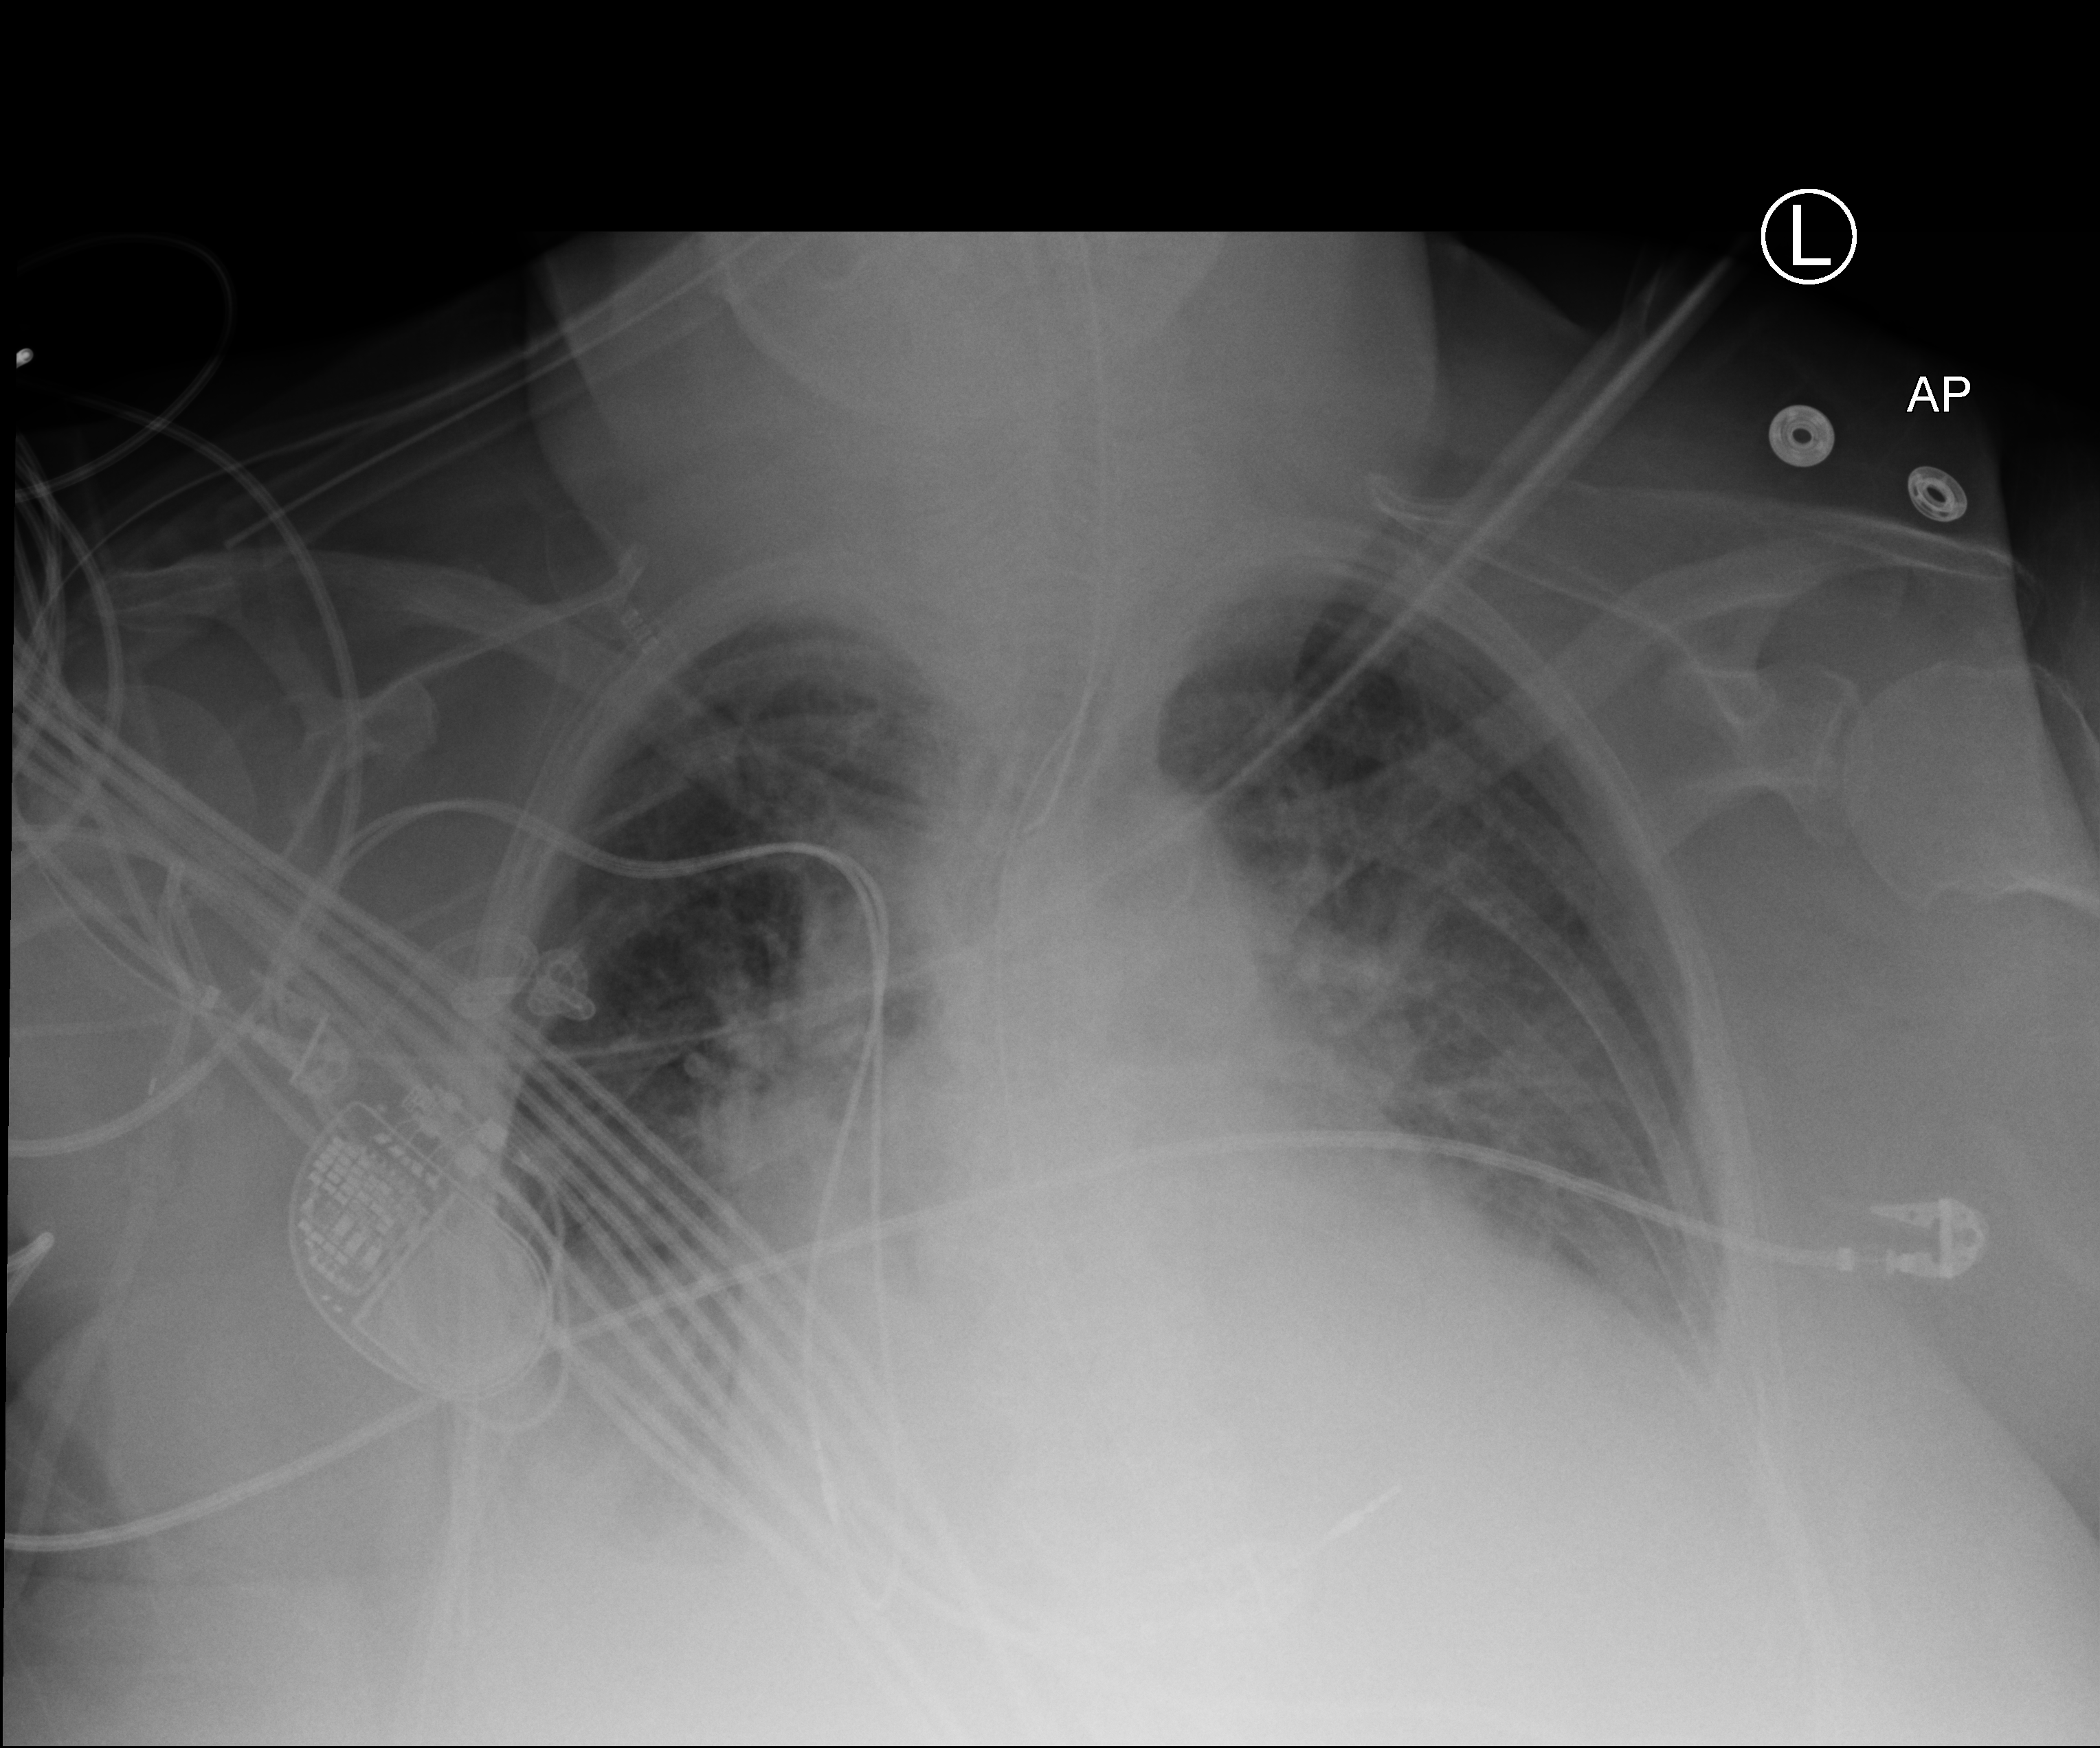
Chest X-ray (portable). Female patient hospitalised with COVID-19, age 75–90 years.
Hospital-stay facts (about this admission, not read from this image; timing relative to this image not recorded):
- admitted to intensive care during this hospital stay: yes
- length of hospital stay: 21 days
- mechanically ventilated during this hospital stay: yes